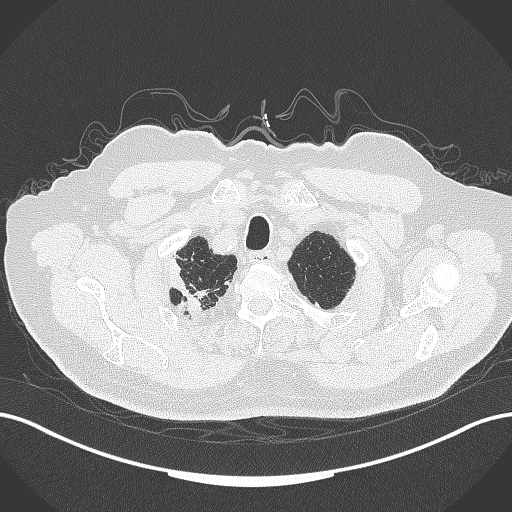
Chest CT, one axial slice; position 329 of 389 along the scan axis; reconstruction kernel B70f; lung window (W 1500 / L -600 HU); 1 mm slice thickness; 512 × 512 image matrix, field of view 400 × 400 mm. Male patient, age 72 years. Case-level facts recorded for this patient, not image findings: clinical TNM (as recorded): T1a N0 M0.
Outlined on this slice (rectangle marked by the reading radiologist):
- lung tumour (recorded histology: squamous cell carcinoma): bounding box (x1, y1, x2, y2) in pixels: (168, 254, 208, 320)